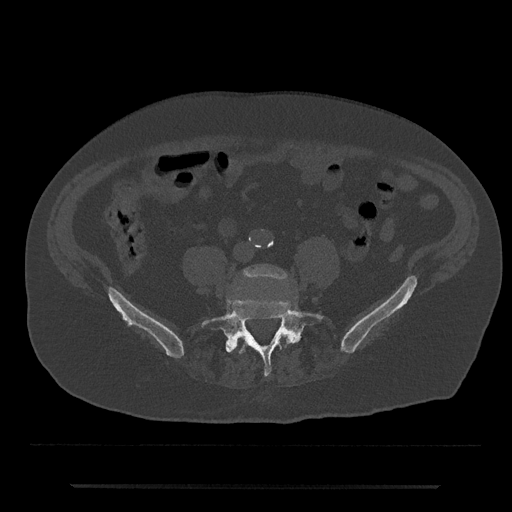
CT including the spine, one axial slice. Slice 303 of 797 in the series (ordered by position). Reconstruction kernel Br40s/3. 120 kVp. Bone window (W 1800 / L 400 HU). 512 × 512 image matrix, field of view 434 × 434 mm. Patient: male, 80 years. From the clinical record (not read from this slice): primary cancer: prostate; vertebrae with lytic lesions (as recorded): L1, T11.
Structures marked on this image (semi-automatically segmented with operator editing):
- L4 vertebra: bounding box <242,265,288,281> (left, top, right, bottom; pixels)
- L5 vertebra: <201,297,323,377>